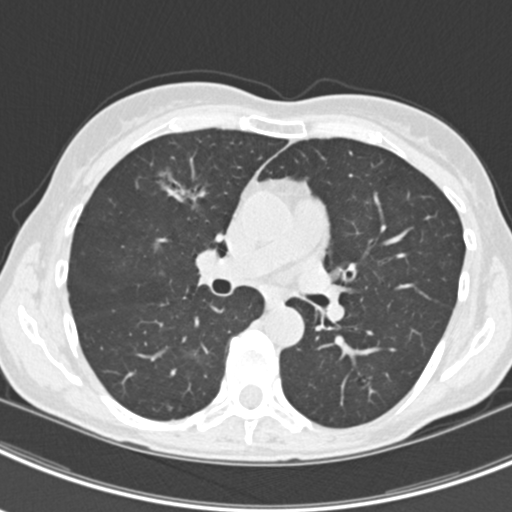
Chest CT (low-dose screening protocol), one axial image. Second screening round (one year after baseline). Lung window (W 1500 / L -600 HU). Slice 84 of 219 in the series. 512 × 512 image matrix, field of view 298 × 298 mm. Female participant, aged 63 years at enrolment. Current smoker at enrolment.
Lesion marked by an expert reader, box from (x=157, y=161) to (x=216, y=215) px. The screening reader recorded 9 non-calcified nodules or masses ≥4 mm on this exam (left upper lobe, right upper lobe, left upper lobe, left lower lobe, right middle lobe, left lower lobe, left lower lobe, right lower lobe, right lower lobe); which of them this box marks is not recorded. Official screen result: positive, other. Lung cancer was diagnosed 408 days after this screen: bronchiolo-alveolar adenocarcinoma, NOS, right upper lobe, right middle lobe, right lower lobe, left upper lobe, left lower lobe, moderately differentiated (G2), stage IV (AJCC 6th edition).